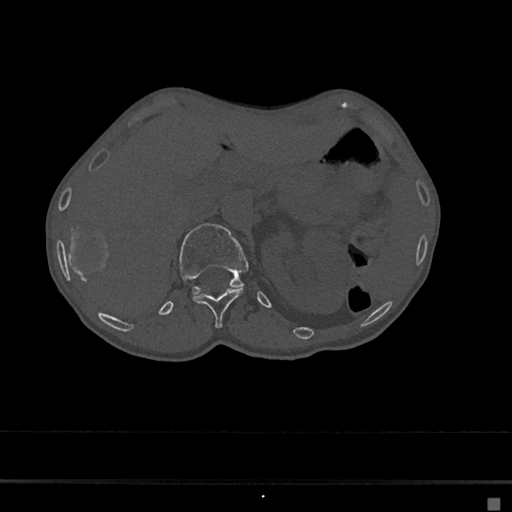
CT including the spine, one axial slice. Slice 98 of 797 in the series (ordered by position). 120 kVp. Bone window (W 1800 / L 400 HU). 512 × 512 image matrix. Female patient, age 68 years. Case-level facts recorded for this patient, not image findings: primary cancer: renal.
Structures marked on this image (semi-automatic segmentation, software-assisted and operator-edited):
- L1 vertebra: box from (x=179, y=223) to (x=250, y=295) px
- T12 vertebra: (x=194, y=288)–(x=243, y=329)